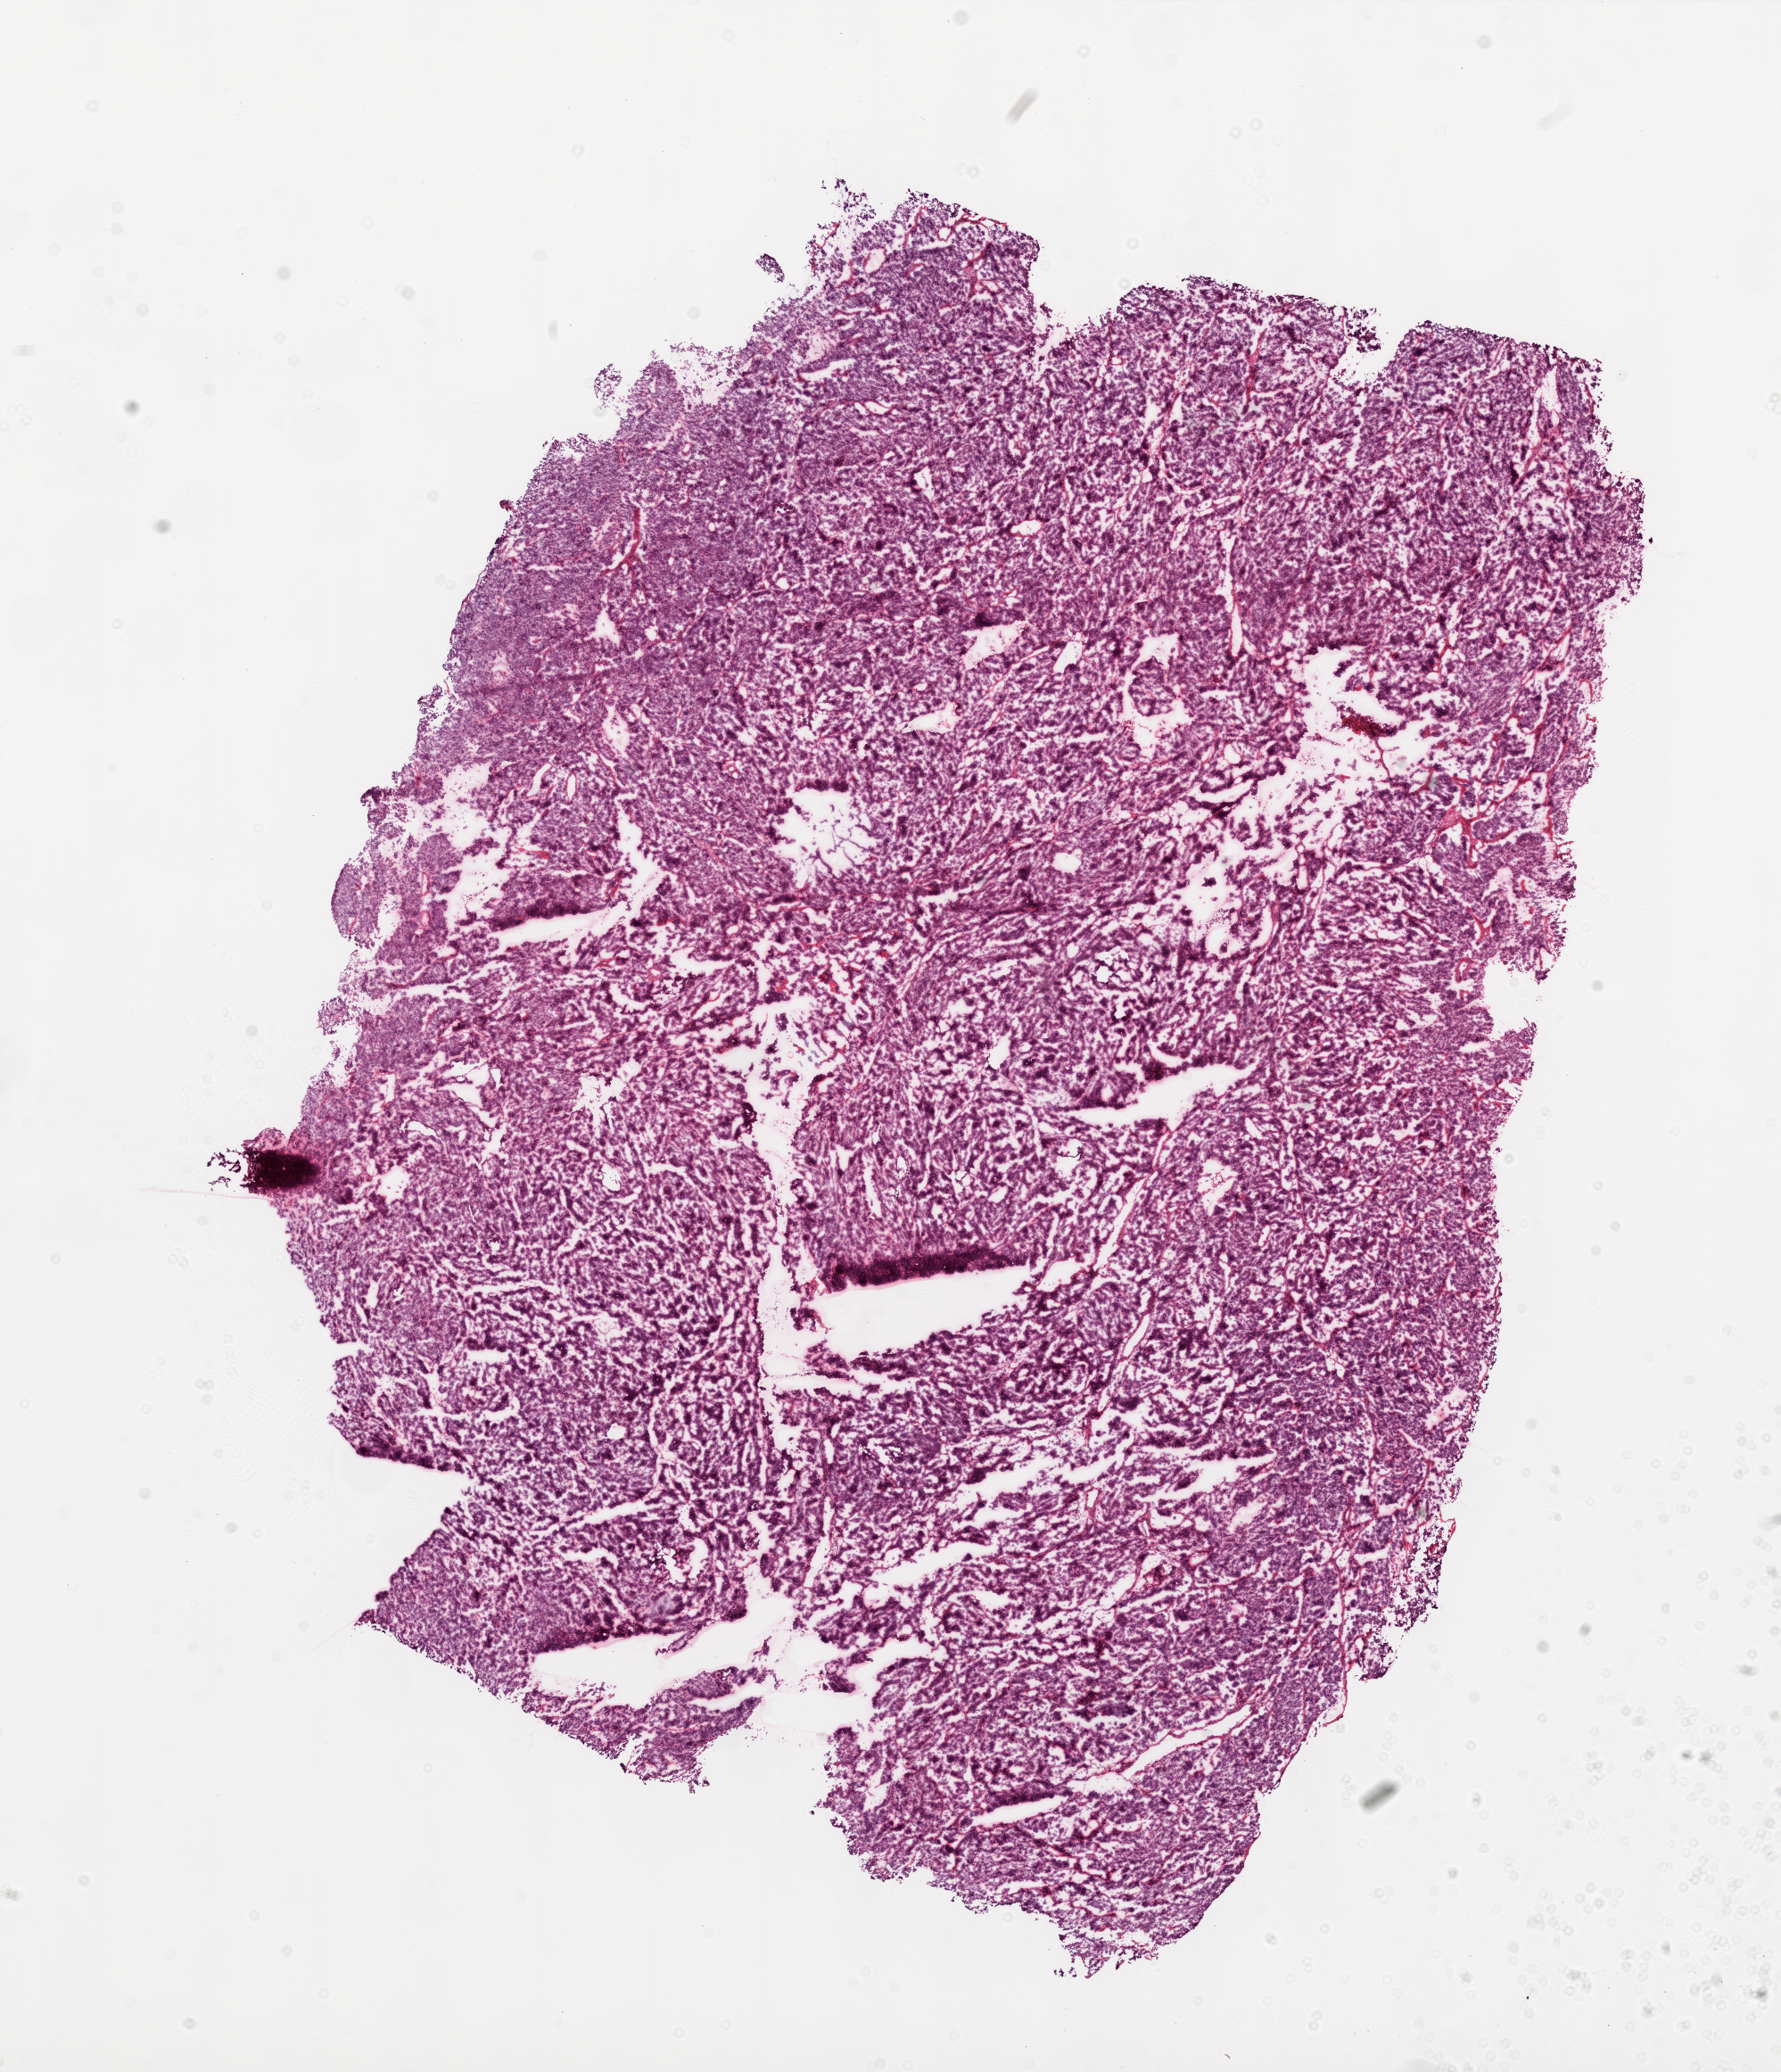
Hematoxylin and eosin (H&E) stained whole-slide image, a low-resolution overview of the entire scanned area, about 16.0 x 18.6 mm (from a 20x scan). Frozen section. Primary tumour sample from the ovary. Female, age 49 years at initial diagnosis. Histologic grade: G3 (poorly differentiated). Composition of this section per pathologist review: tumour cells 95%, tumour nuclei 98%, normal cells 0%, stromal cells 5%, necrosis 0%.
FIGO stage: IIIC. Diagnosis: Serous cystadenocarcinoma, NOS.